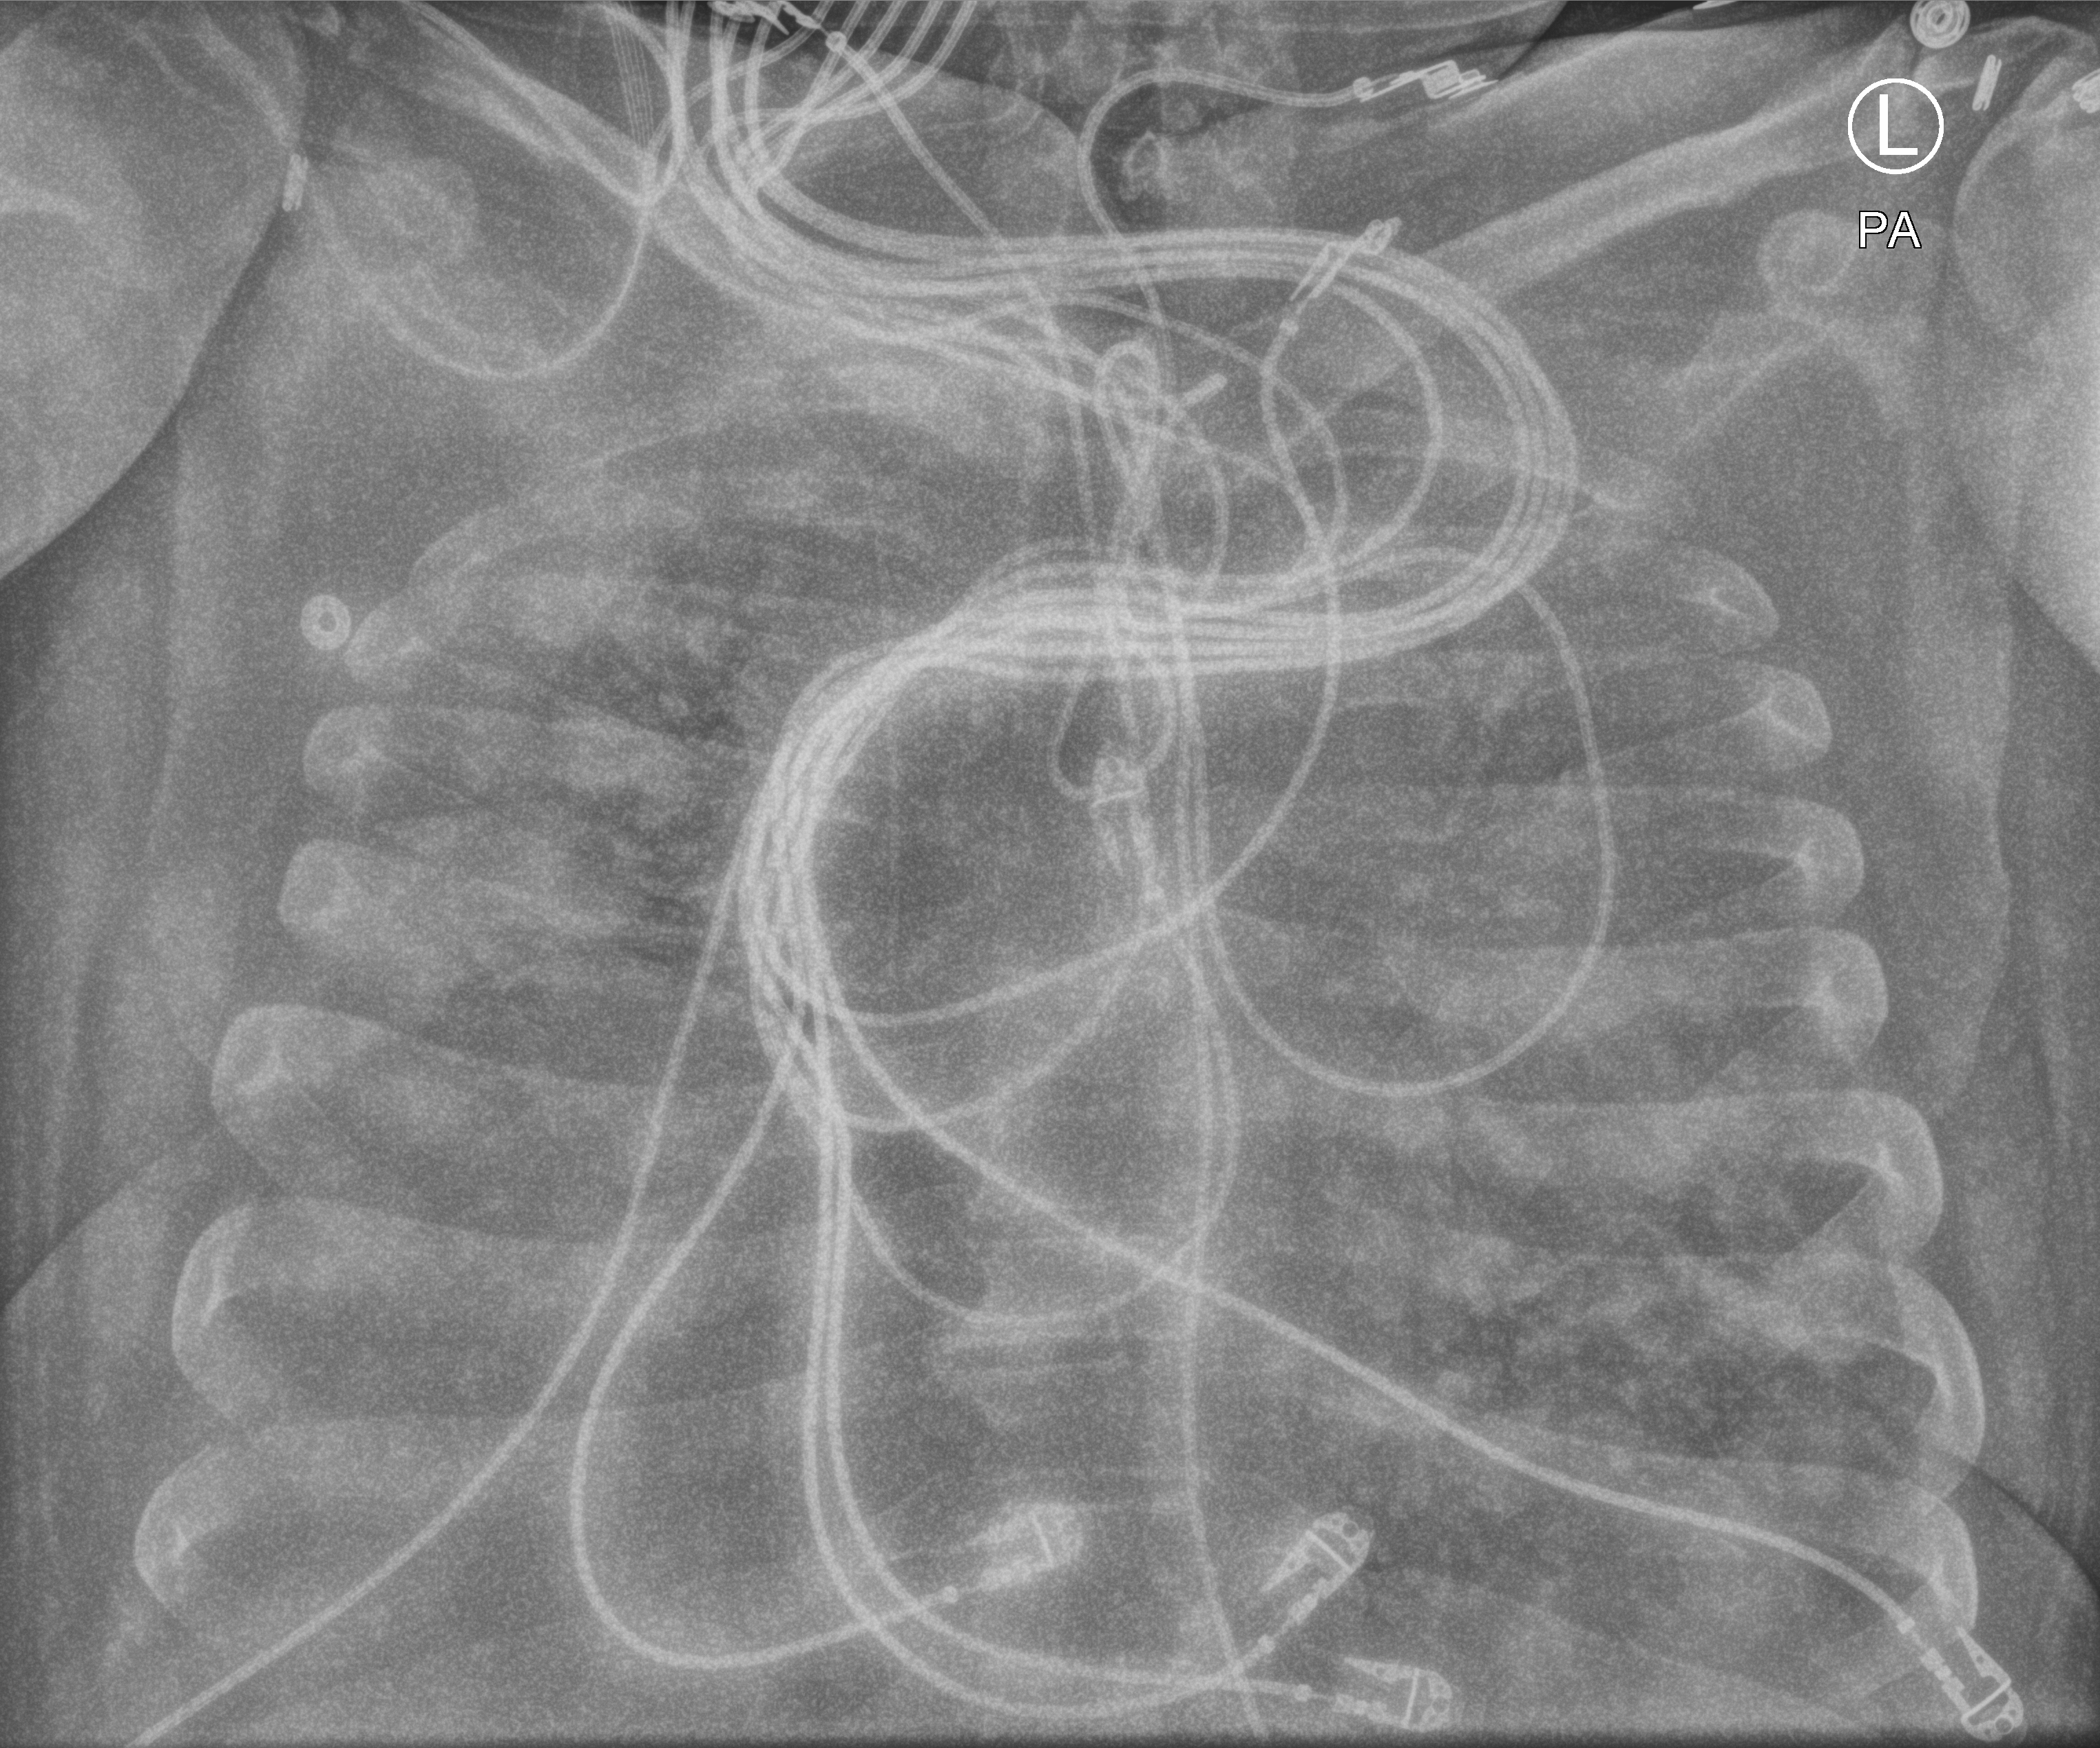
Chest X-ray (portable). Patient hospitalised with COVID-19, aged 18–59 years.
From the hospital-stay record, not from the radiograph (when in the stay this image was taken is not recorded): length of hospital stay: 10 days; admitted to intensive care during this hospital stay: yes.